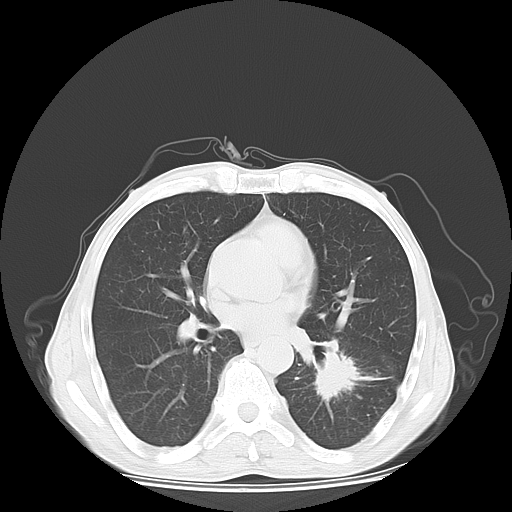
Chest CT, one axial slice; position 32 of 65 along the scan axis; reconstruction kernel LUNG; 120 kVp; lung window (W 1500 / L -600 HU); 5 mm slice thickness; 512 × 512 image matrix, field of view 350 × 350 mm. Male patient, age 63 years. From the clinical record (not read from this slice): clinical TNM (as recorded): T1c N0 M1b.
Annotated regions visible in this slice (bounding box drawn by a radiologist):
- lung tumour (recorded histology: adenocarcinoma): bounding box (x1, y1, x2, y2) in pixels: (294, 339, 369, 409)